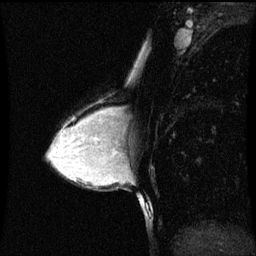
Breast MRI (dynamic contrast-enhanced), one sagittal slice; position 38 of 60 along the scan axis; dynamic contrast-enhanced series, image 2 of 3 at this slice position (ordered by acquisition); 1.5 T; TE 4.2 ms, TR 8.9 ms; 256 × 256 image matrix. Female patient, age 33 years. From the clinical record (not read from this slice): setting: breast cancer imaged before/during neoadjuvant chemotherapy; receptor status: HER2-positive.
Outlined on this slice (semi-automatically segmented with operator editing):
- analysis volume of interest (the breast-tissue region the enhancement analysis was run in; not a lesion): bounding box (x1, y1, x2, y2) in pixels: (107, 108, 122, 147)
- tumour enhancement mask (voxels above the 70 % enhancement threshold inside the analysis volume of interest): (107, 108, 116, 117)